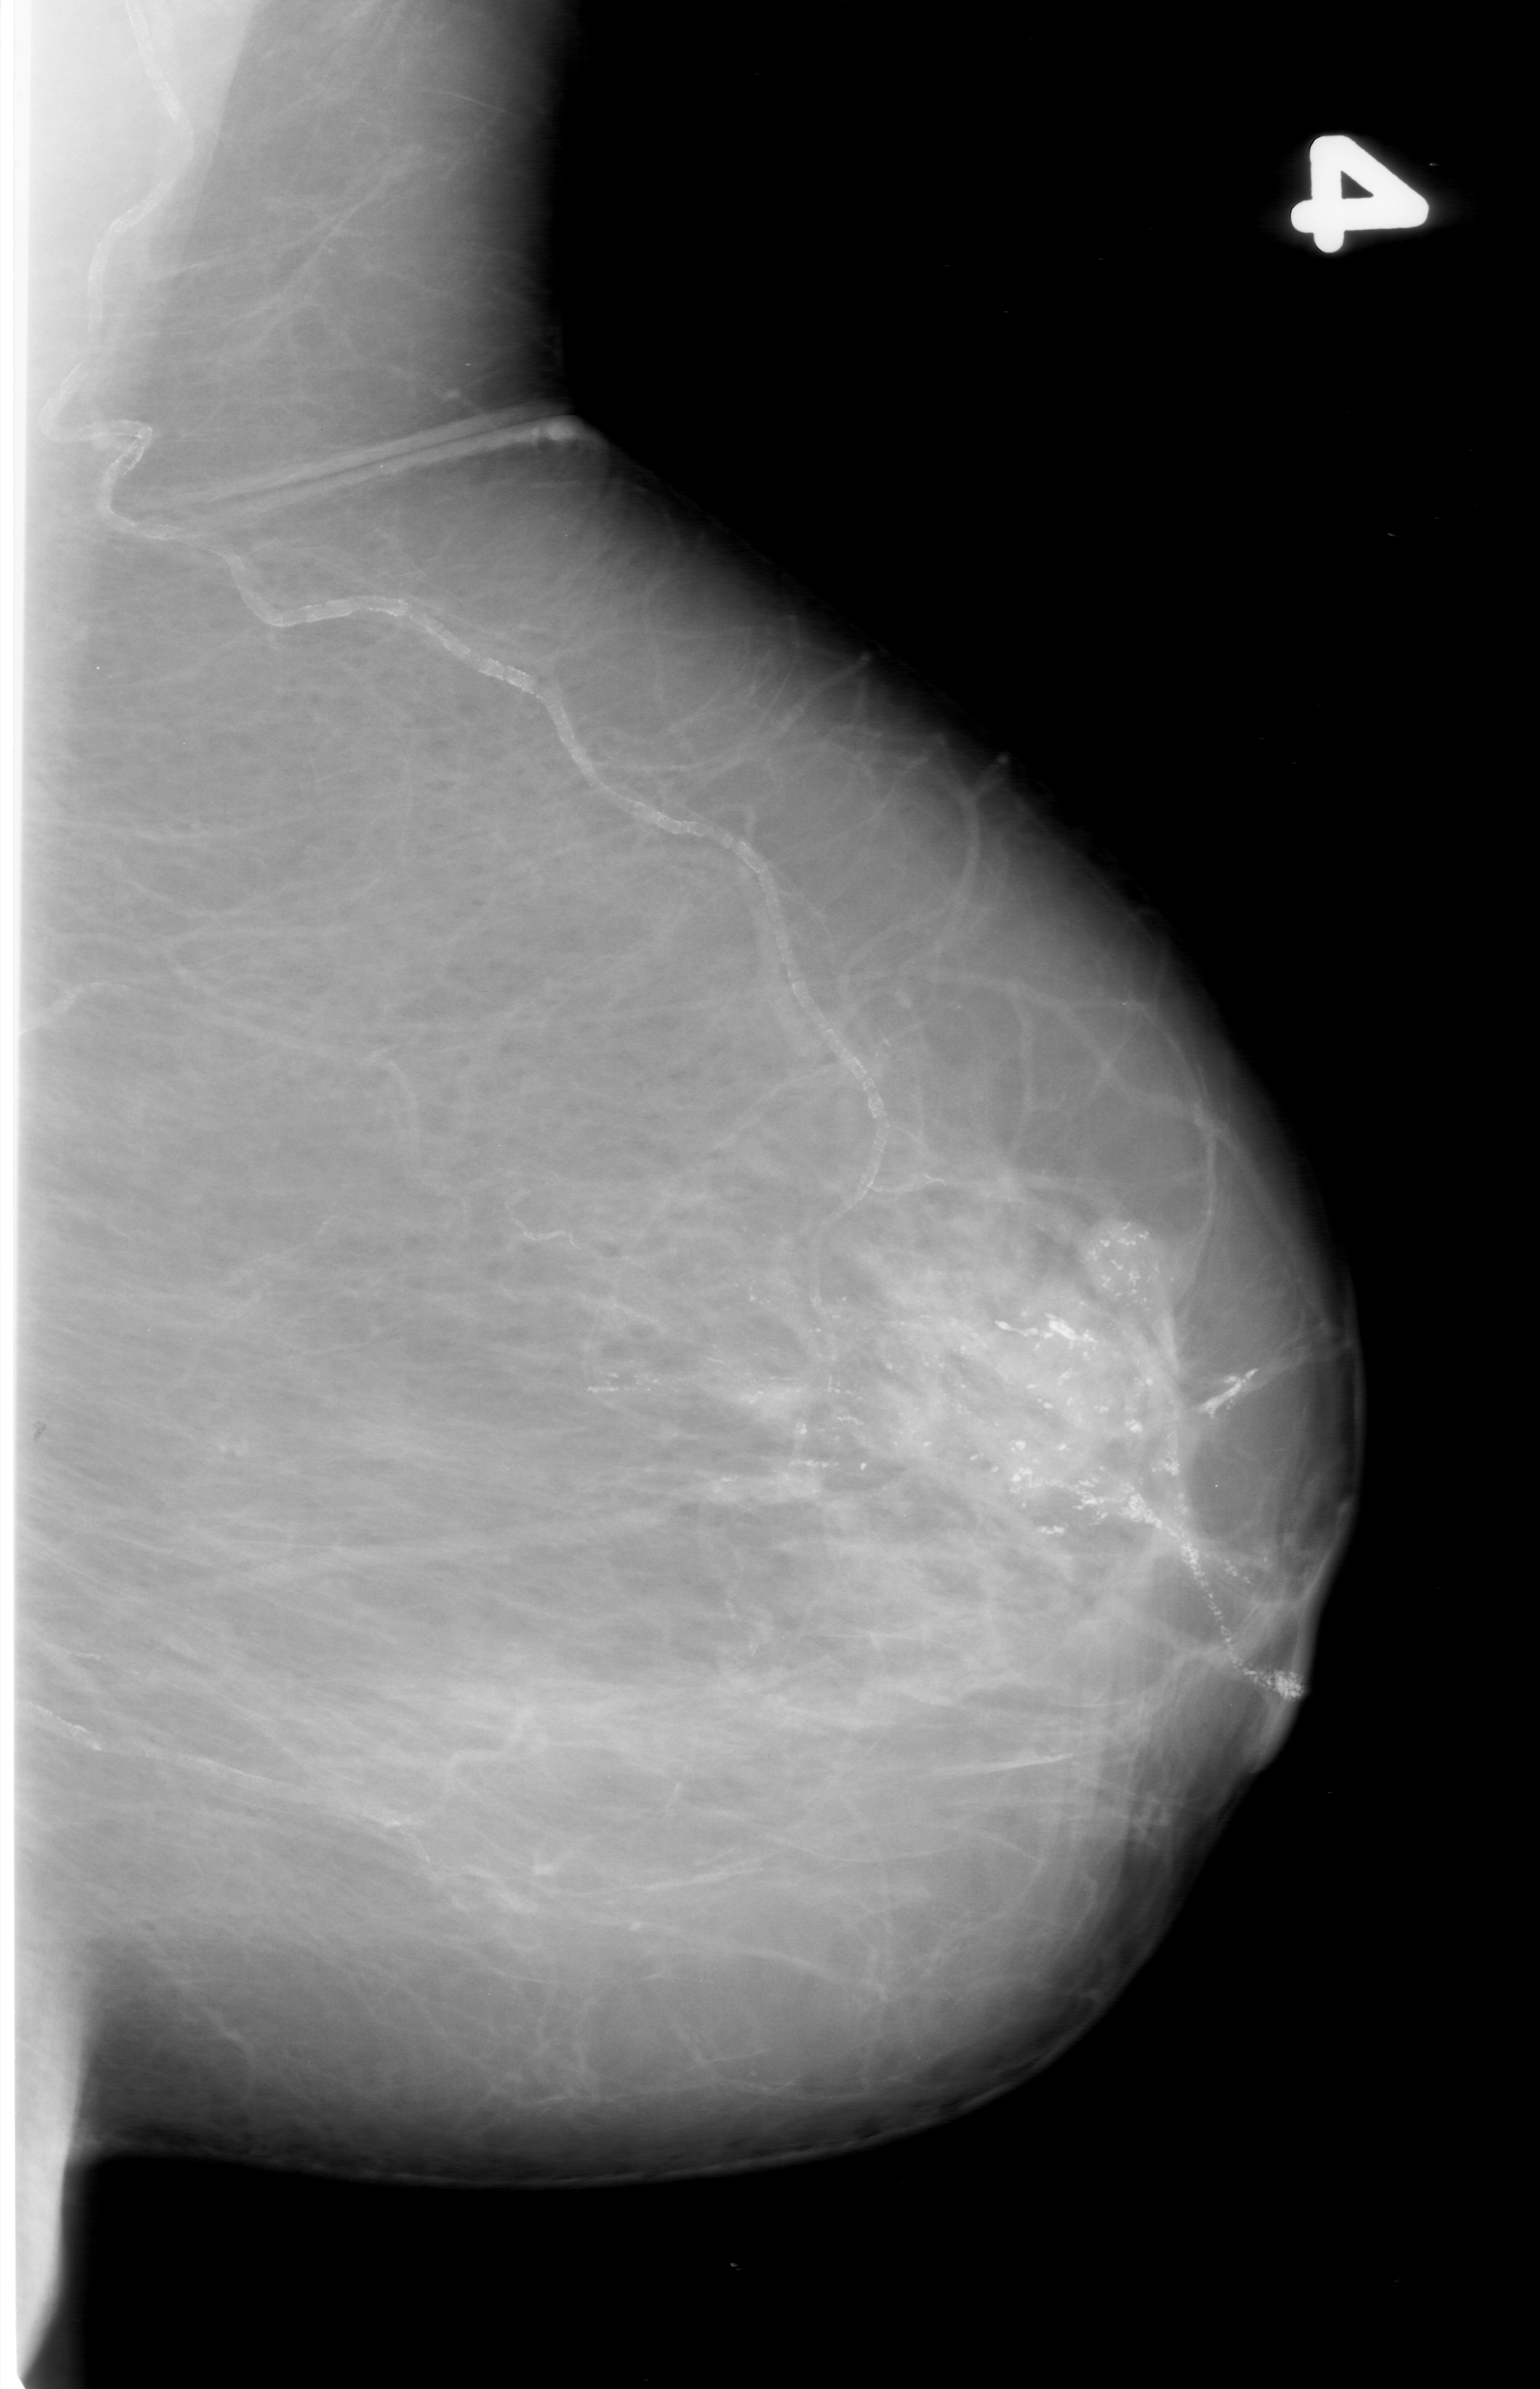
Digitized screen-film mammogram; left breast; MLO view; BI-RADS breast density category 1 (scale 1–4).
Marked abnormality: calcifications, morphology pleomorphic, distribution linear; BI-RADS assessment category 5; subtlety rating 5 on a 1 (subtle) to 5 (obvious) scale; pathology result (as recorded, not read from the image): malignant.